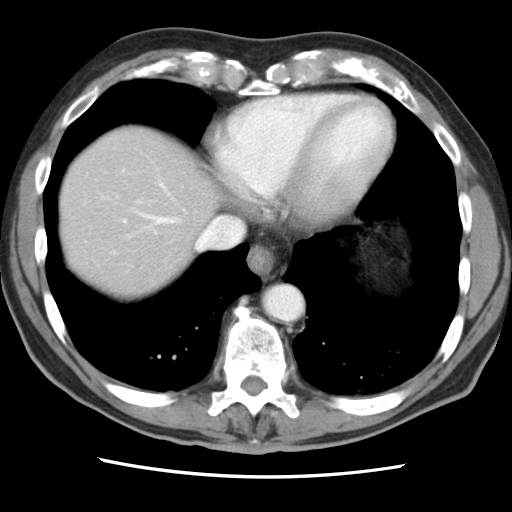
Contrast-enhanced abdominal CT, one axial slice; slice 76 of 83 in the series (ordered by position); 120 kVp; intravenous contrast given; soft-tissue window (W 400 / L 40 HU); 512 × 512 image matrix. Male patient, age 69 years. From the clinical record (not read from this slice): diagnosis: colorectal cancer liver metastases, imaged before liver resection; multiple liver metastases: yes; largest metastasis: 3.5 cm; disease in both lobes: no.
Annotated regions visible in this slice (manually delineated by an expert):
- hepatic veins: box from (x=139, y=213) to (x=243, y=250) px
- liver: (x=60, y=124)–(x=217, y=299)
- planned liver remnant (the part of the liver to remain after resection): (x=60, y=155)–(x=212, y=299)
- portal vein (with intrahepatic branches): (x=123, y=220)–(x=126, y=223)